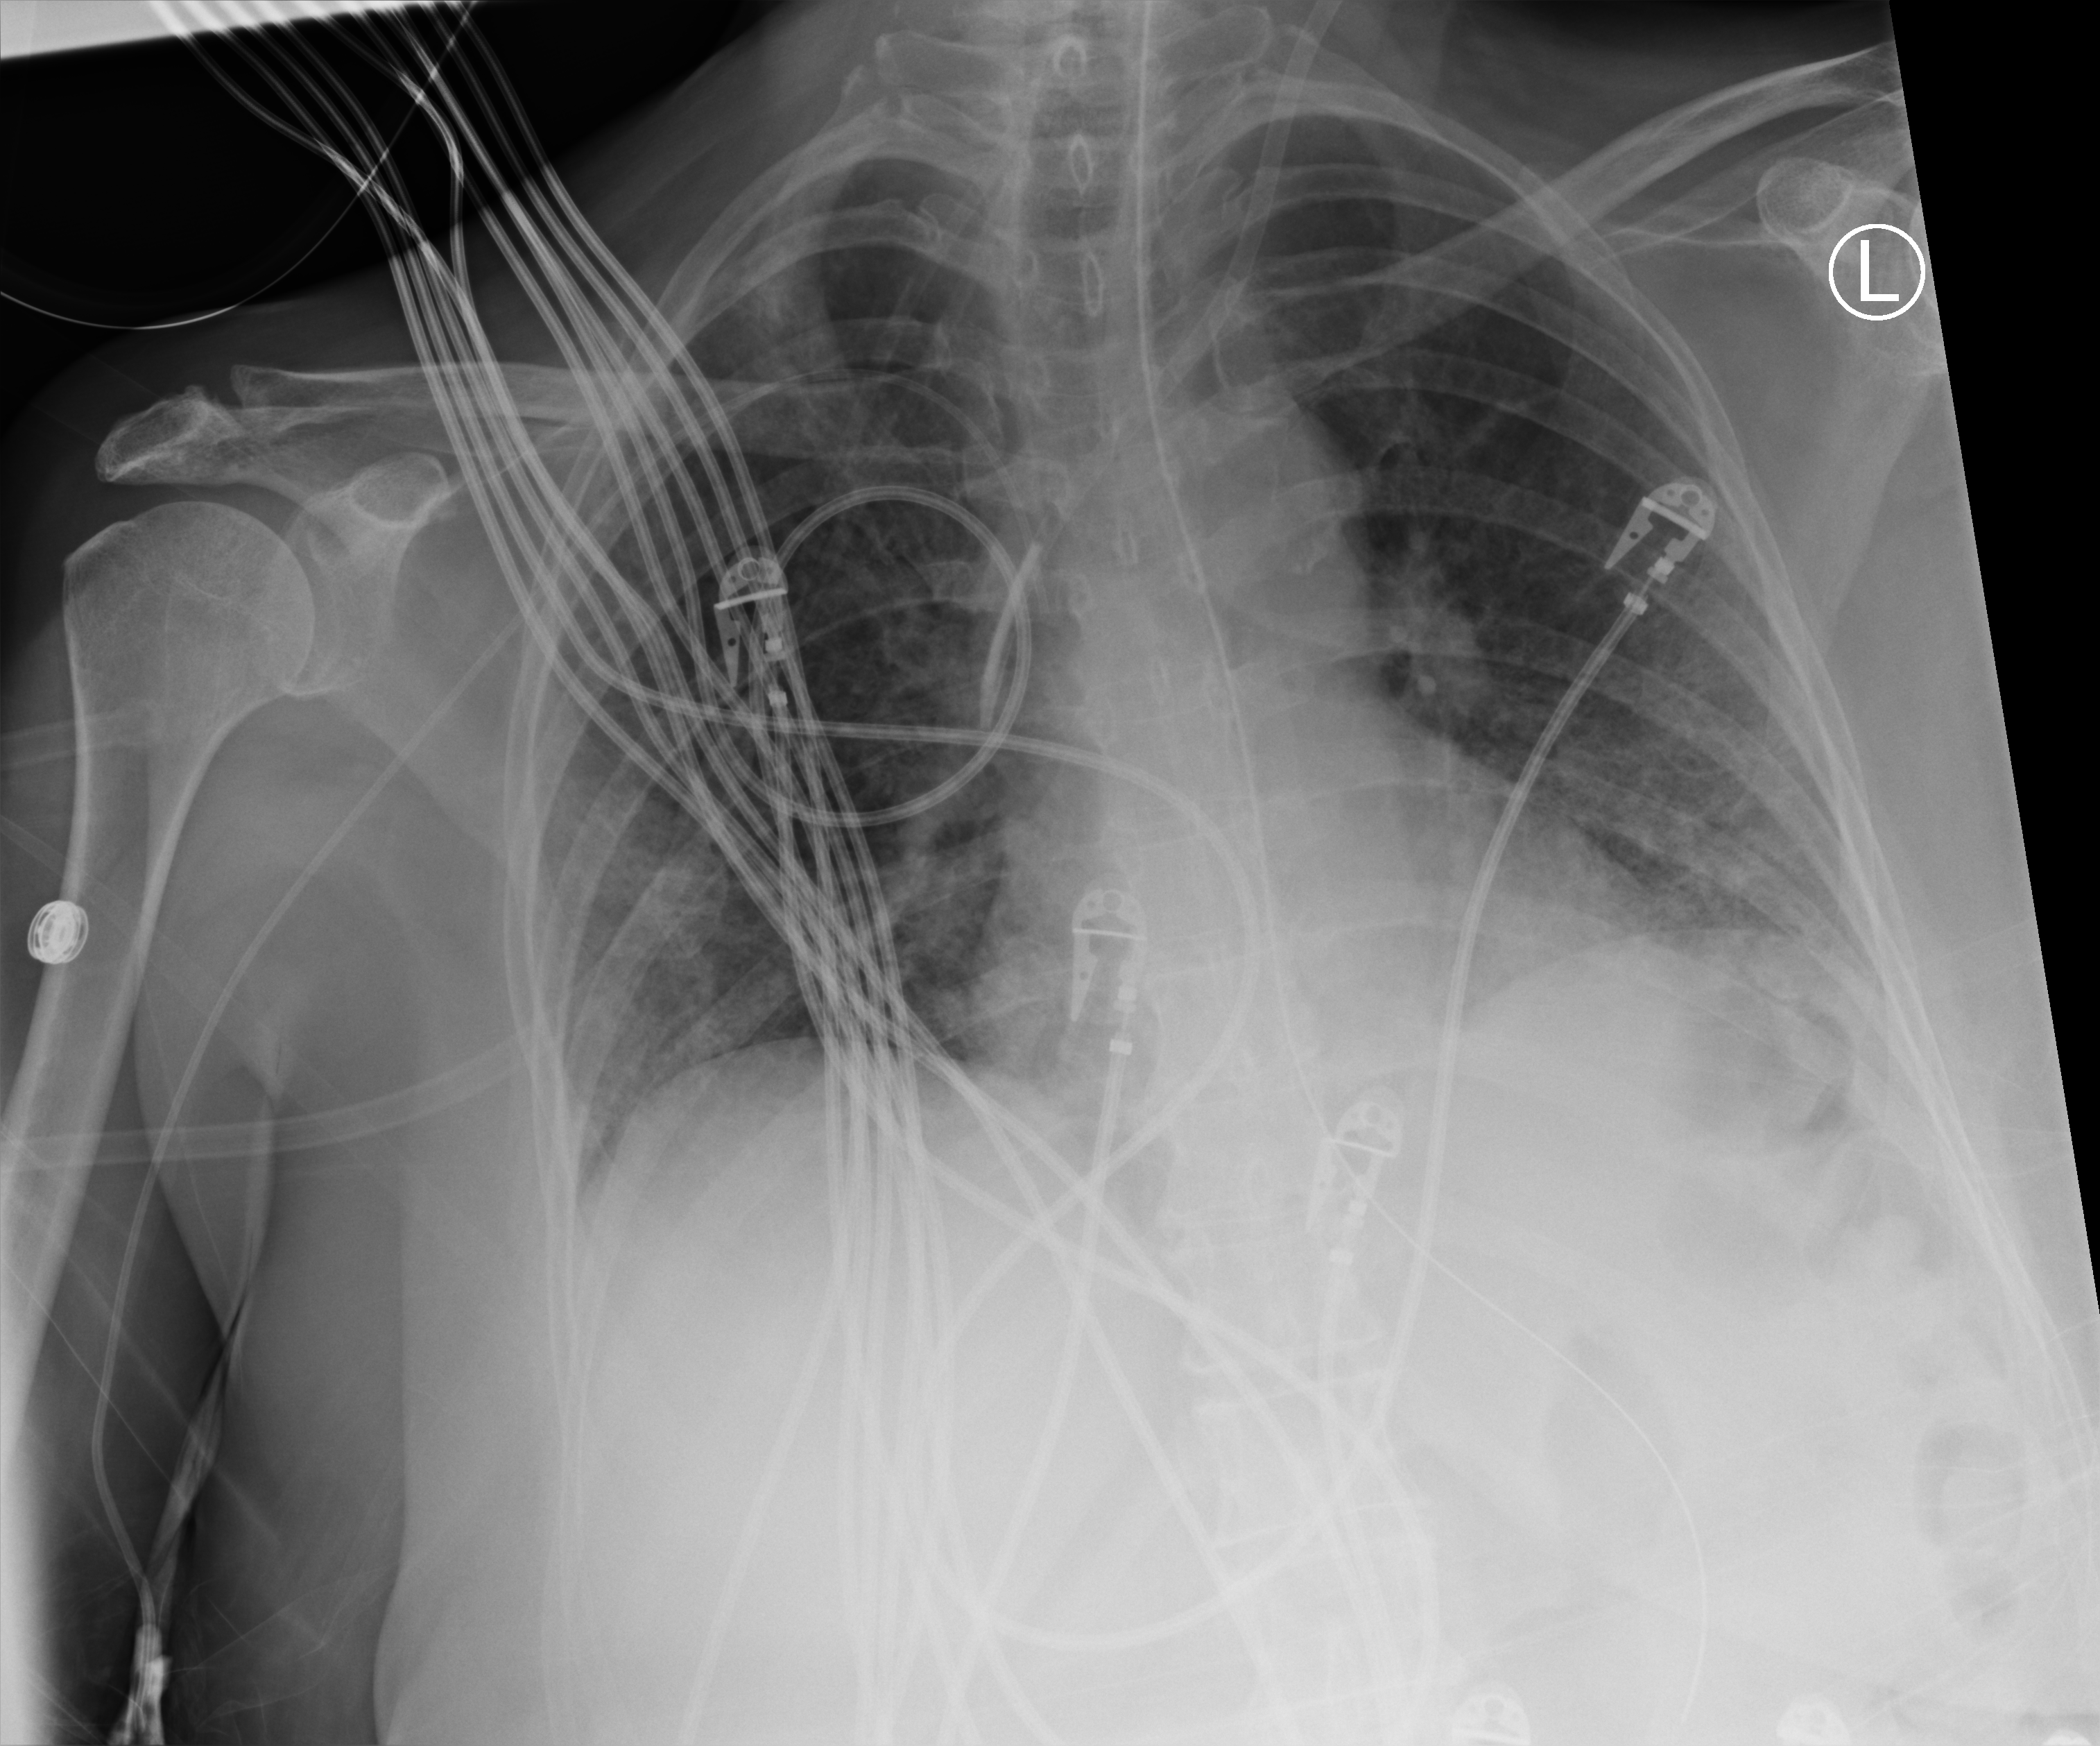
Chest X-ray (portable); anteroposterior (AP) projection. Female patient hospitalised with COVID-19, age 60–74 years.
Hospital-stay facts (about this admission, not read from this image; timing relative to this image not recorded): hypertension (admission record): yes; mechanically ventilated during this hospital stay: yes.